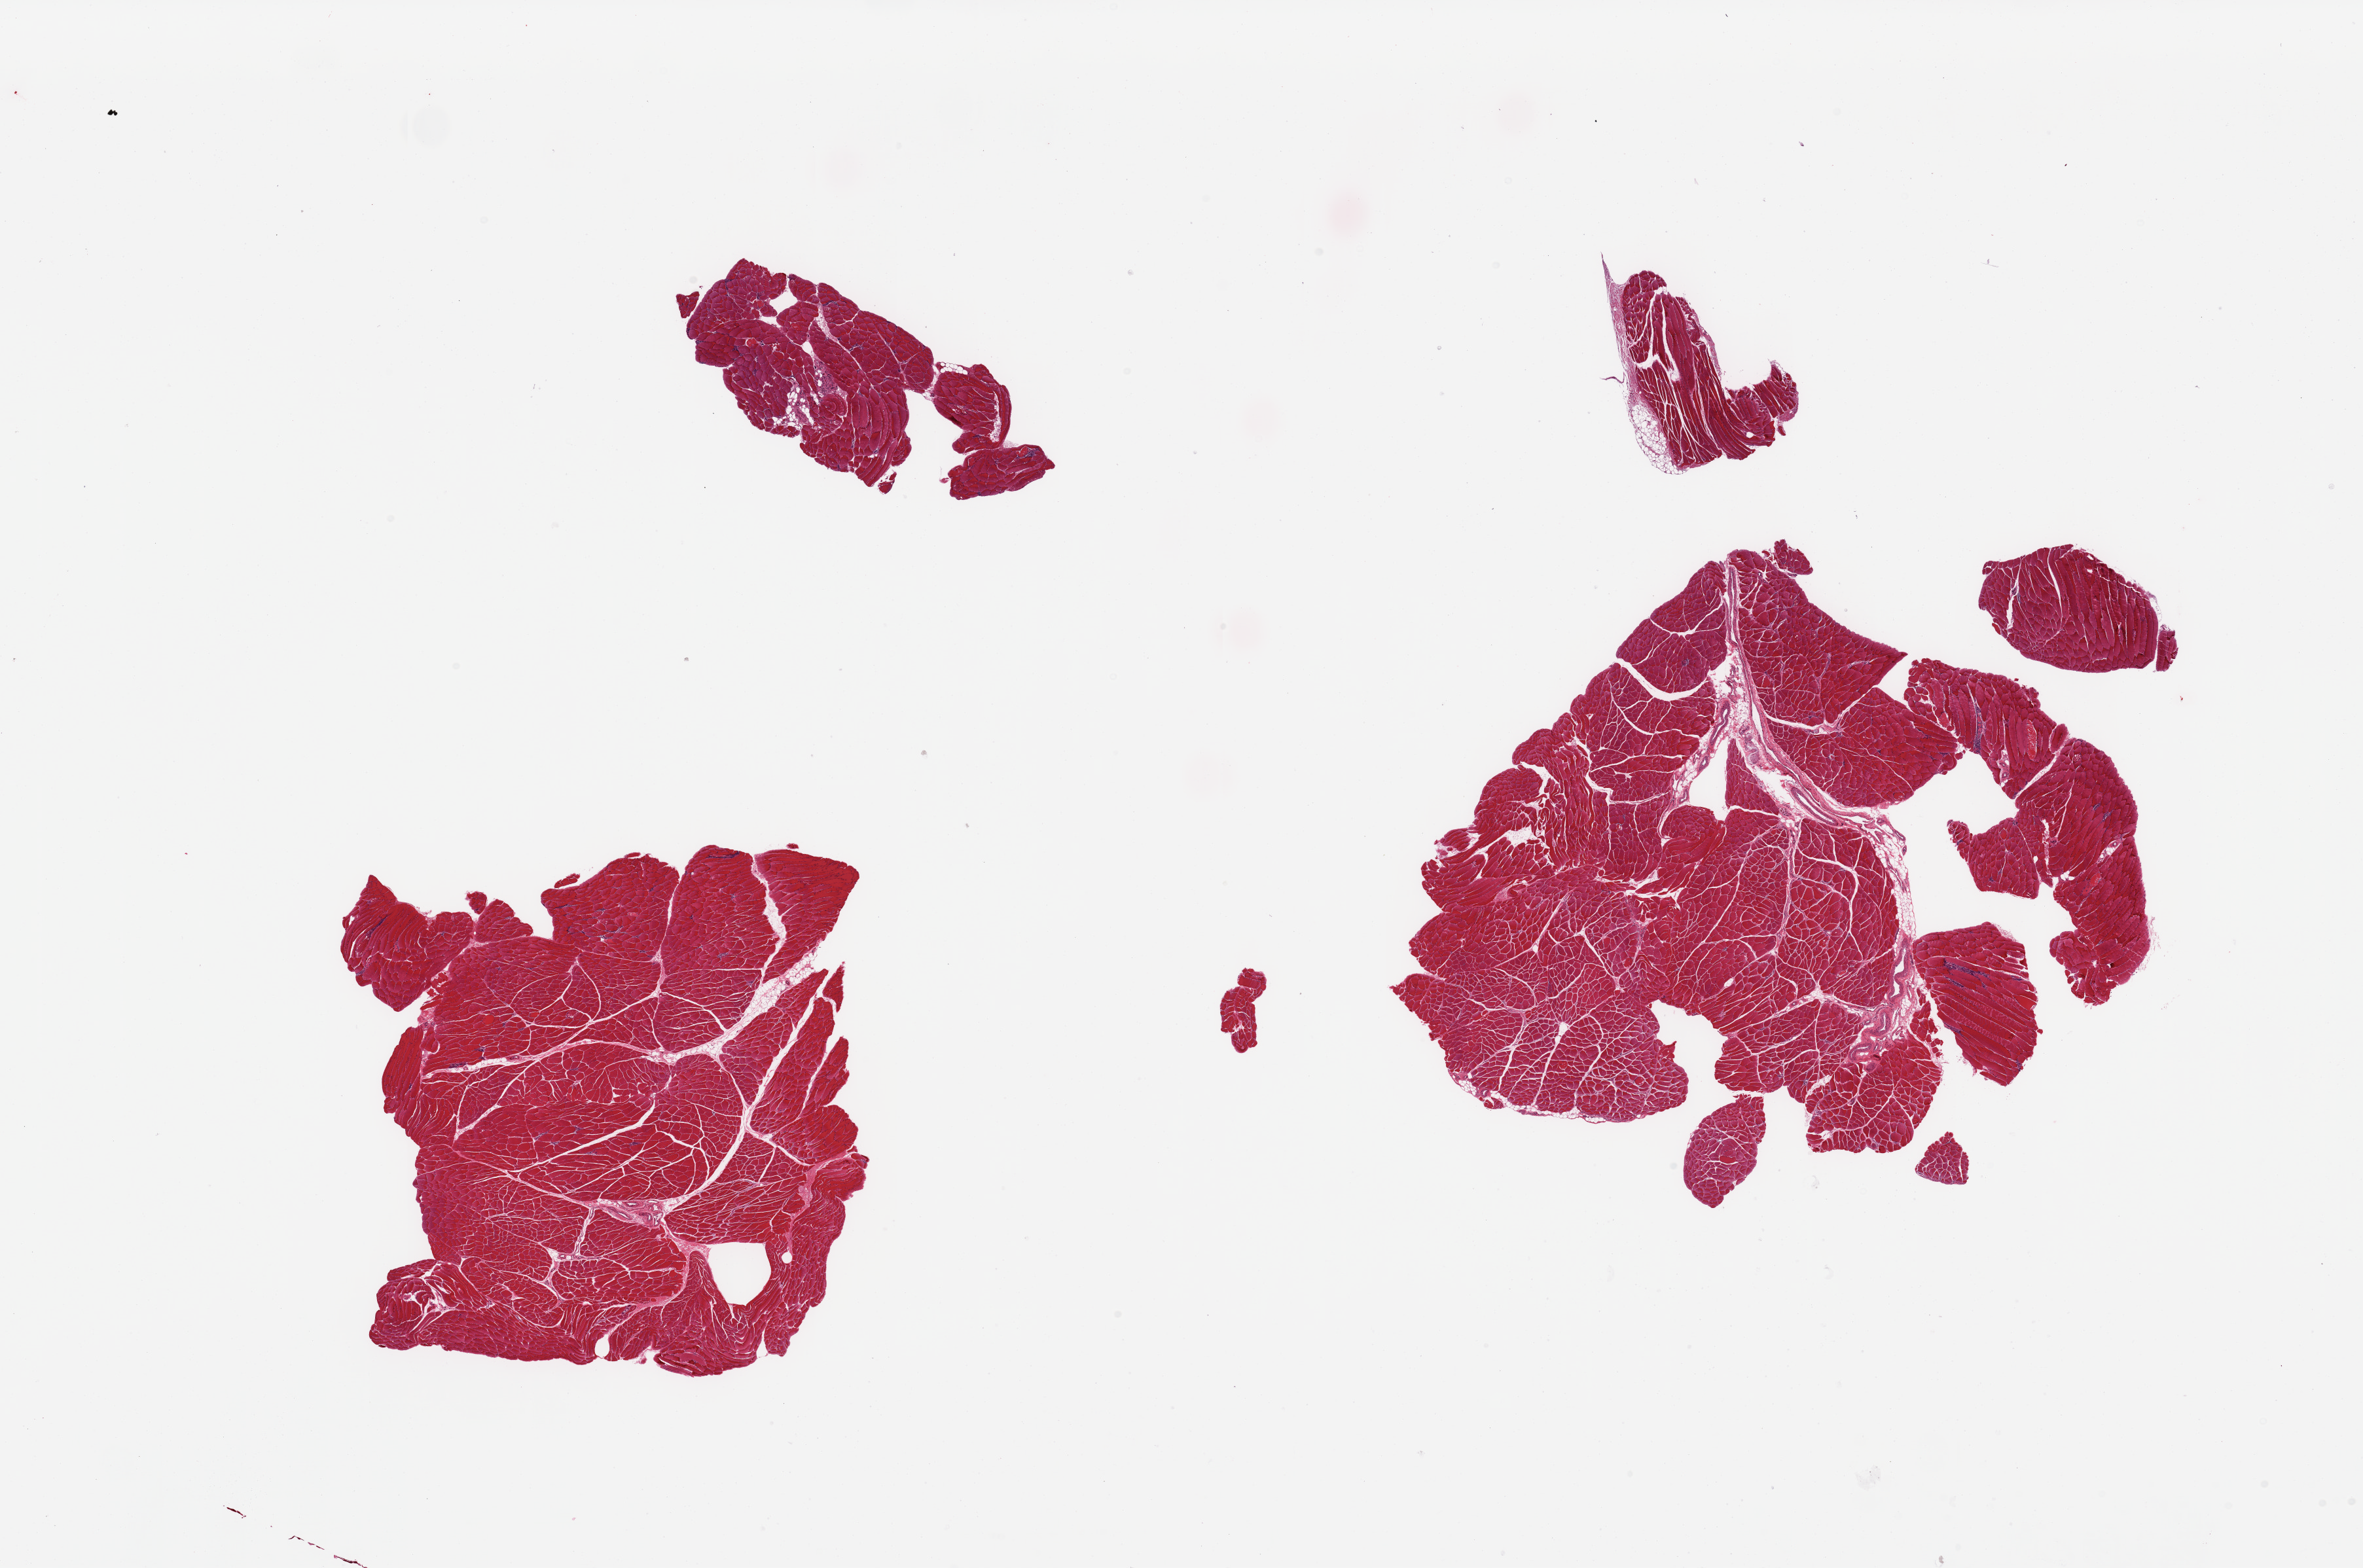
Digitized hematoxylin and eosin (H&E)-stained section, brightfield, shown as a low-resolution overview of the whole scanned area (about 28.5 x 18.9 mm). PAXgene-fixed paraffin-embedded (PFPE) section. Sampled site (target tissue): skeletal muscle. Donor tissue sample.
* pathologist's review note for this sample: 2 pieces (fragmented); ~10% interstitial fat/vascular elements; few foci of inflammatory myositis